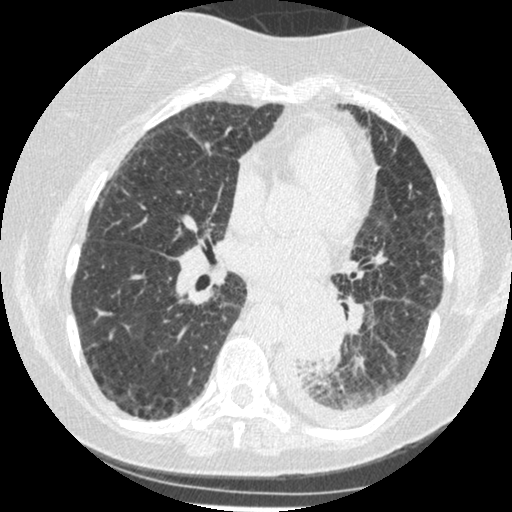
Low-dose screening chest CT, one axial slice; position 112 of 341 along the scan axis; reconstruction kernel STANDARD; lung window (W 1500 / L -600 HU); 1.25 mm slice thickness; 512 × 512 image matrix, field of view 310 × 310 mm.
Annotated regions visible in this slice (expert manual segmentation):
- lesion 1 (tumor, lower lobe of left lung): bounding box [x1, y1, x2, y2] px = [284, 302, 340, 363]